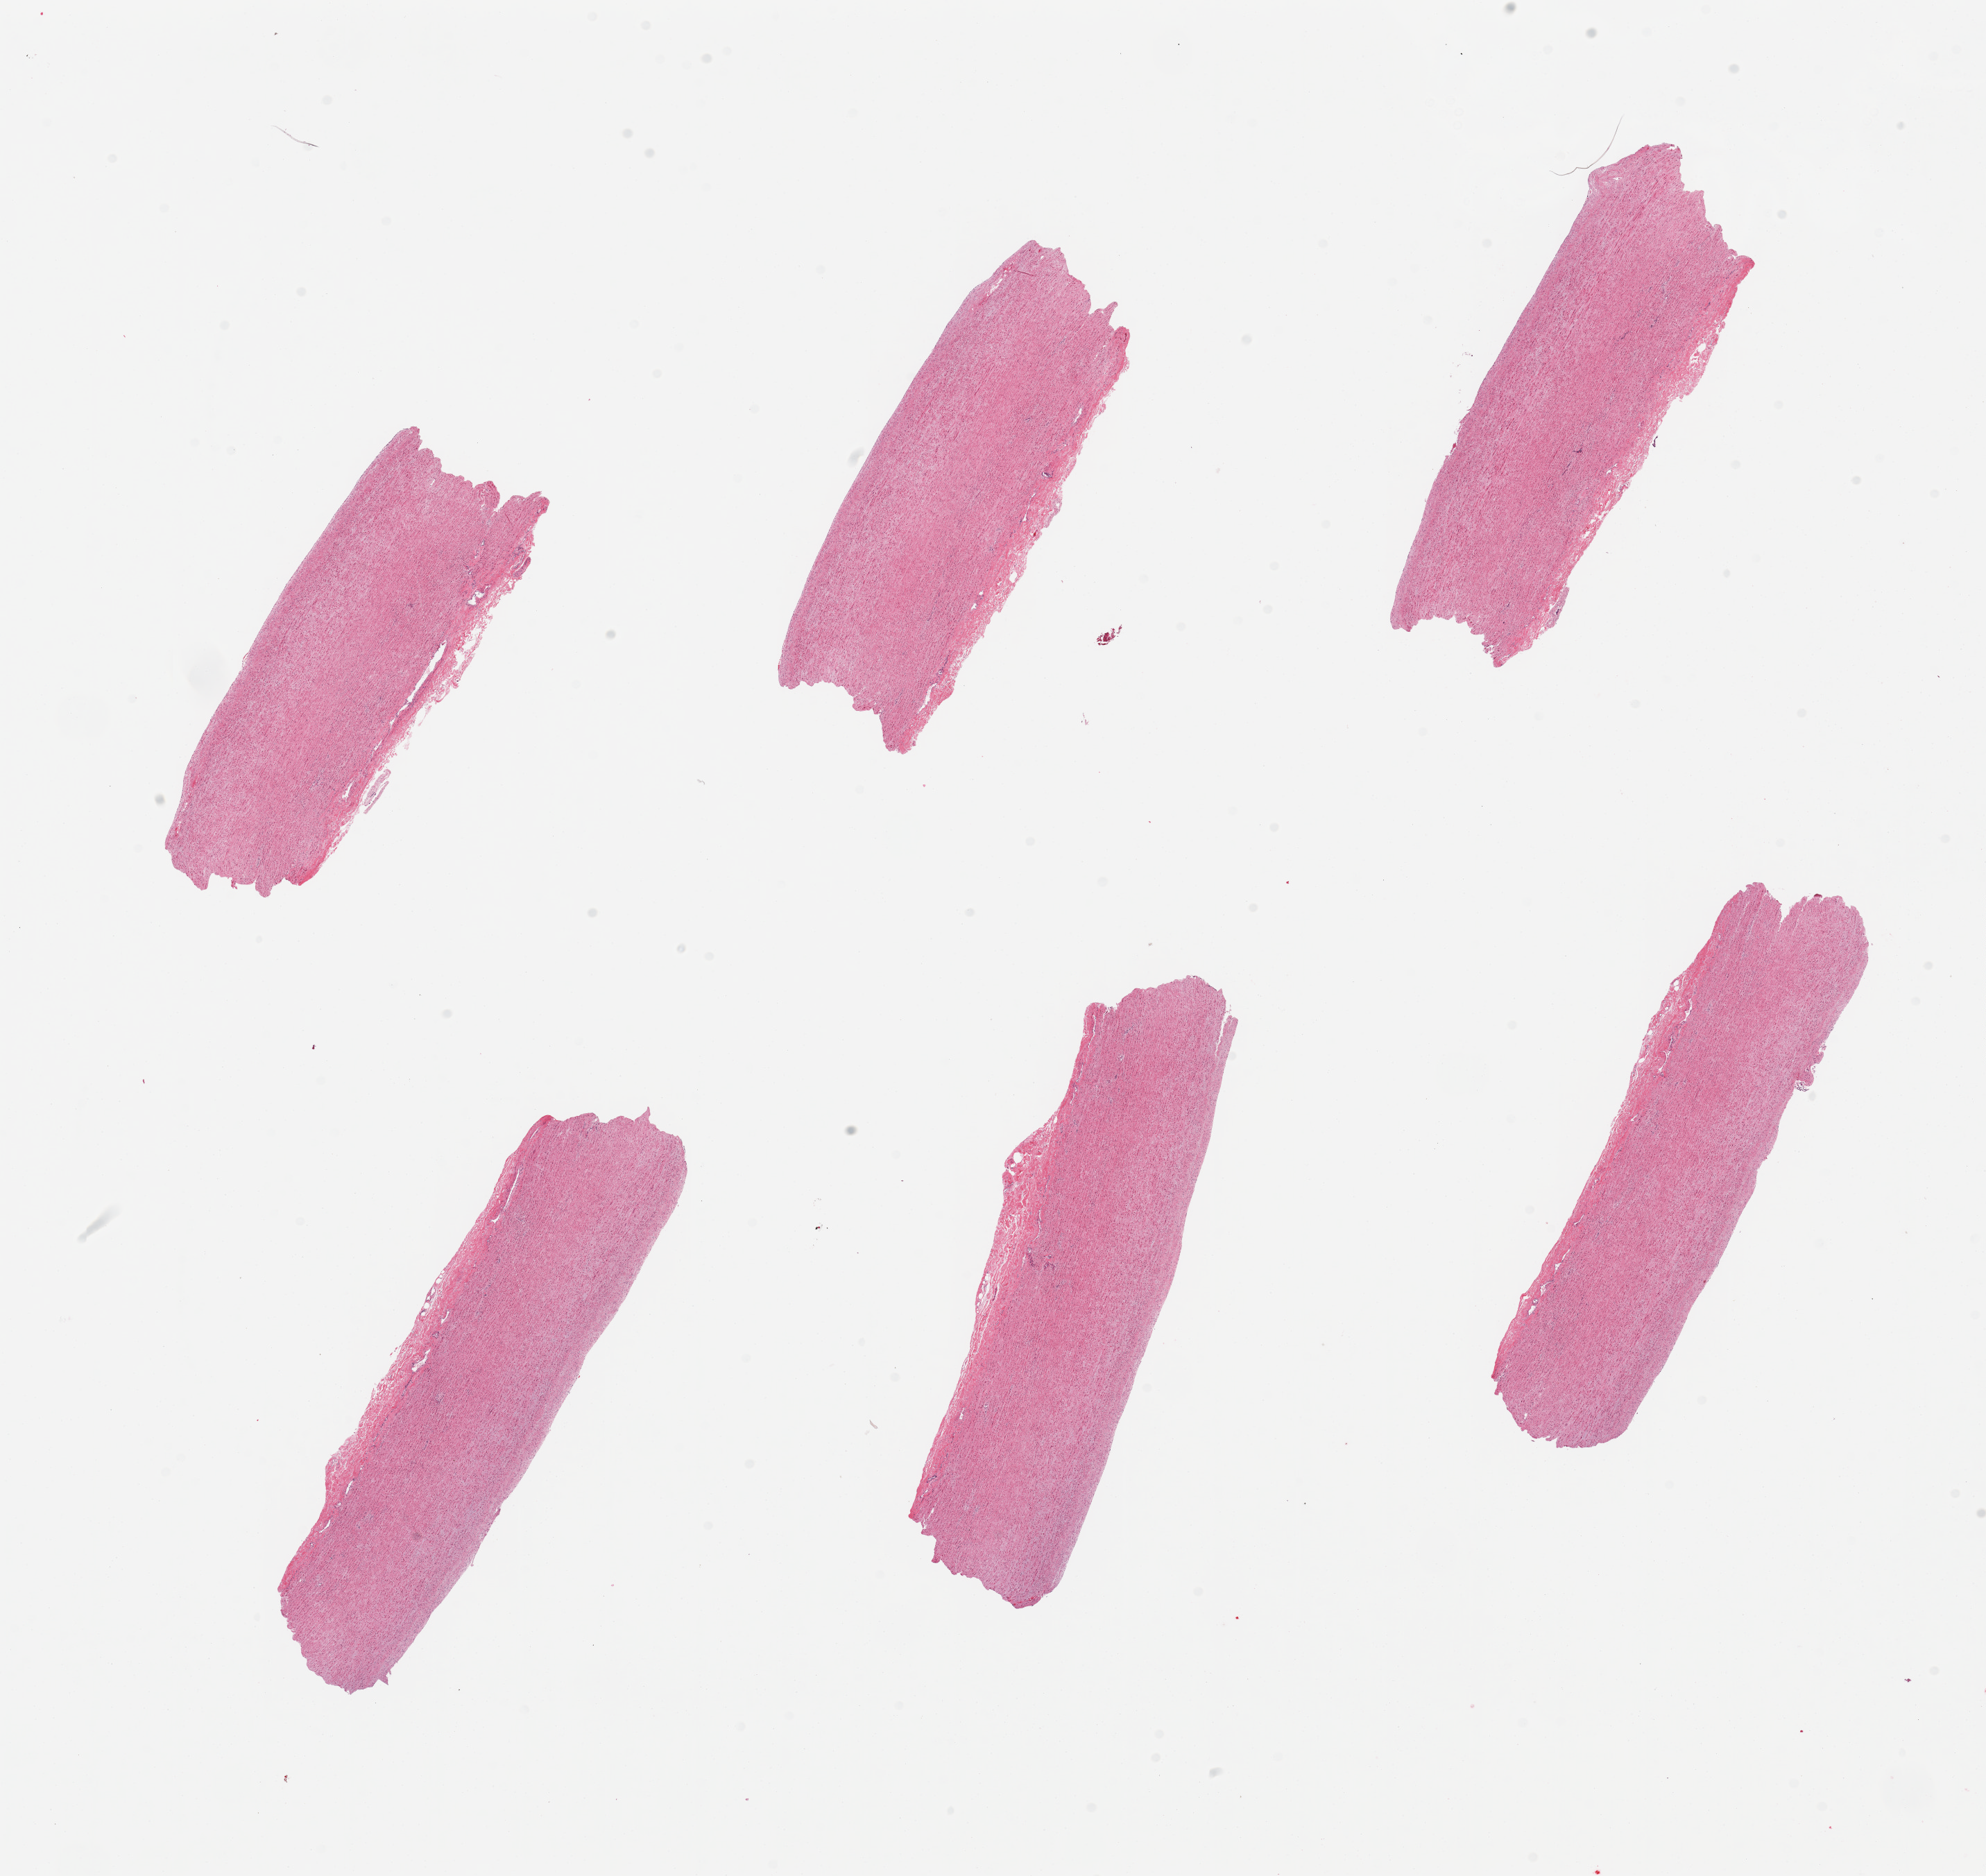
Whole-slide image, H&E stain — whole scanned area (about 22.6 x 21.4 mm) shown as a low-resolution overview, PAXgene-fixed, paraffin-embedded tissue, sampled site (target tissue): aorta, donor tissue sample.
Review note (as recorded): 6 pieces, no abnormalties.